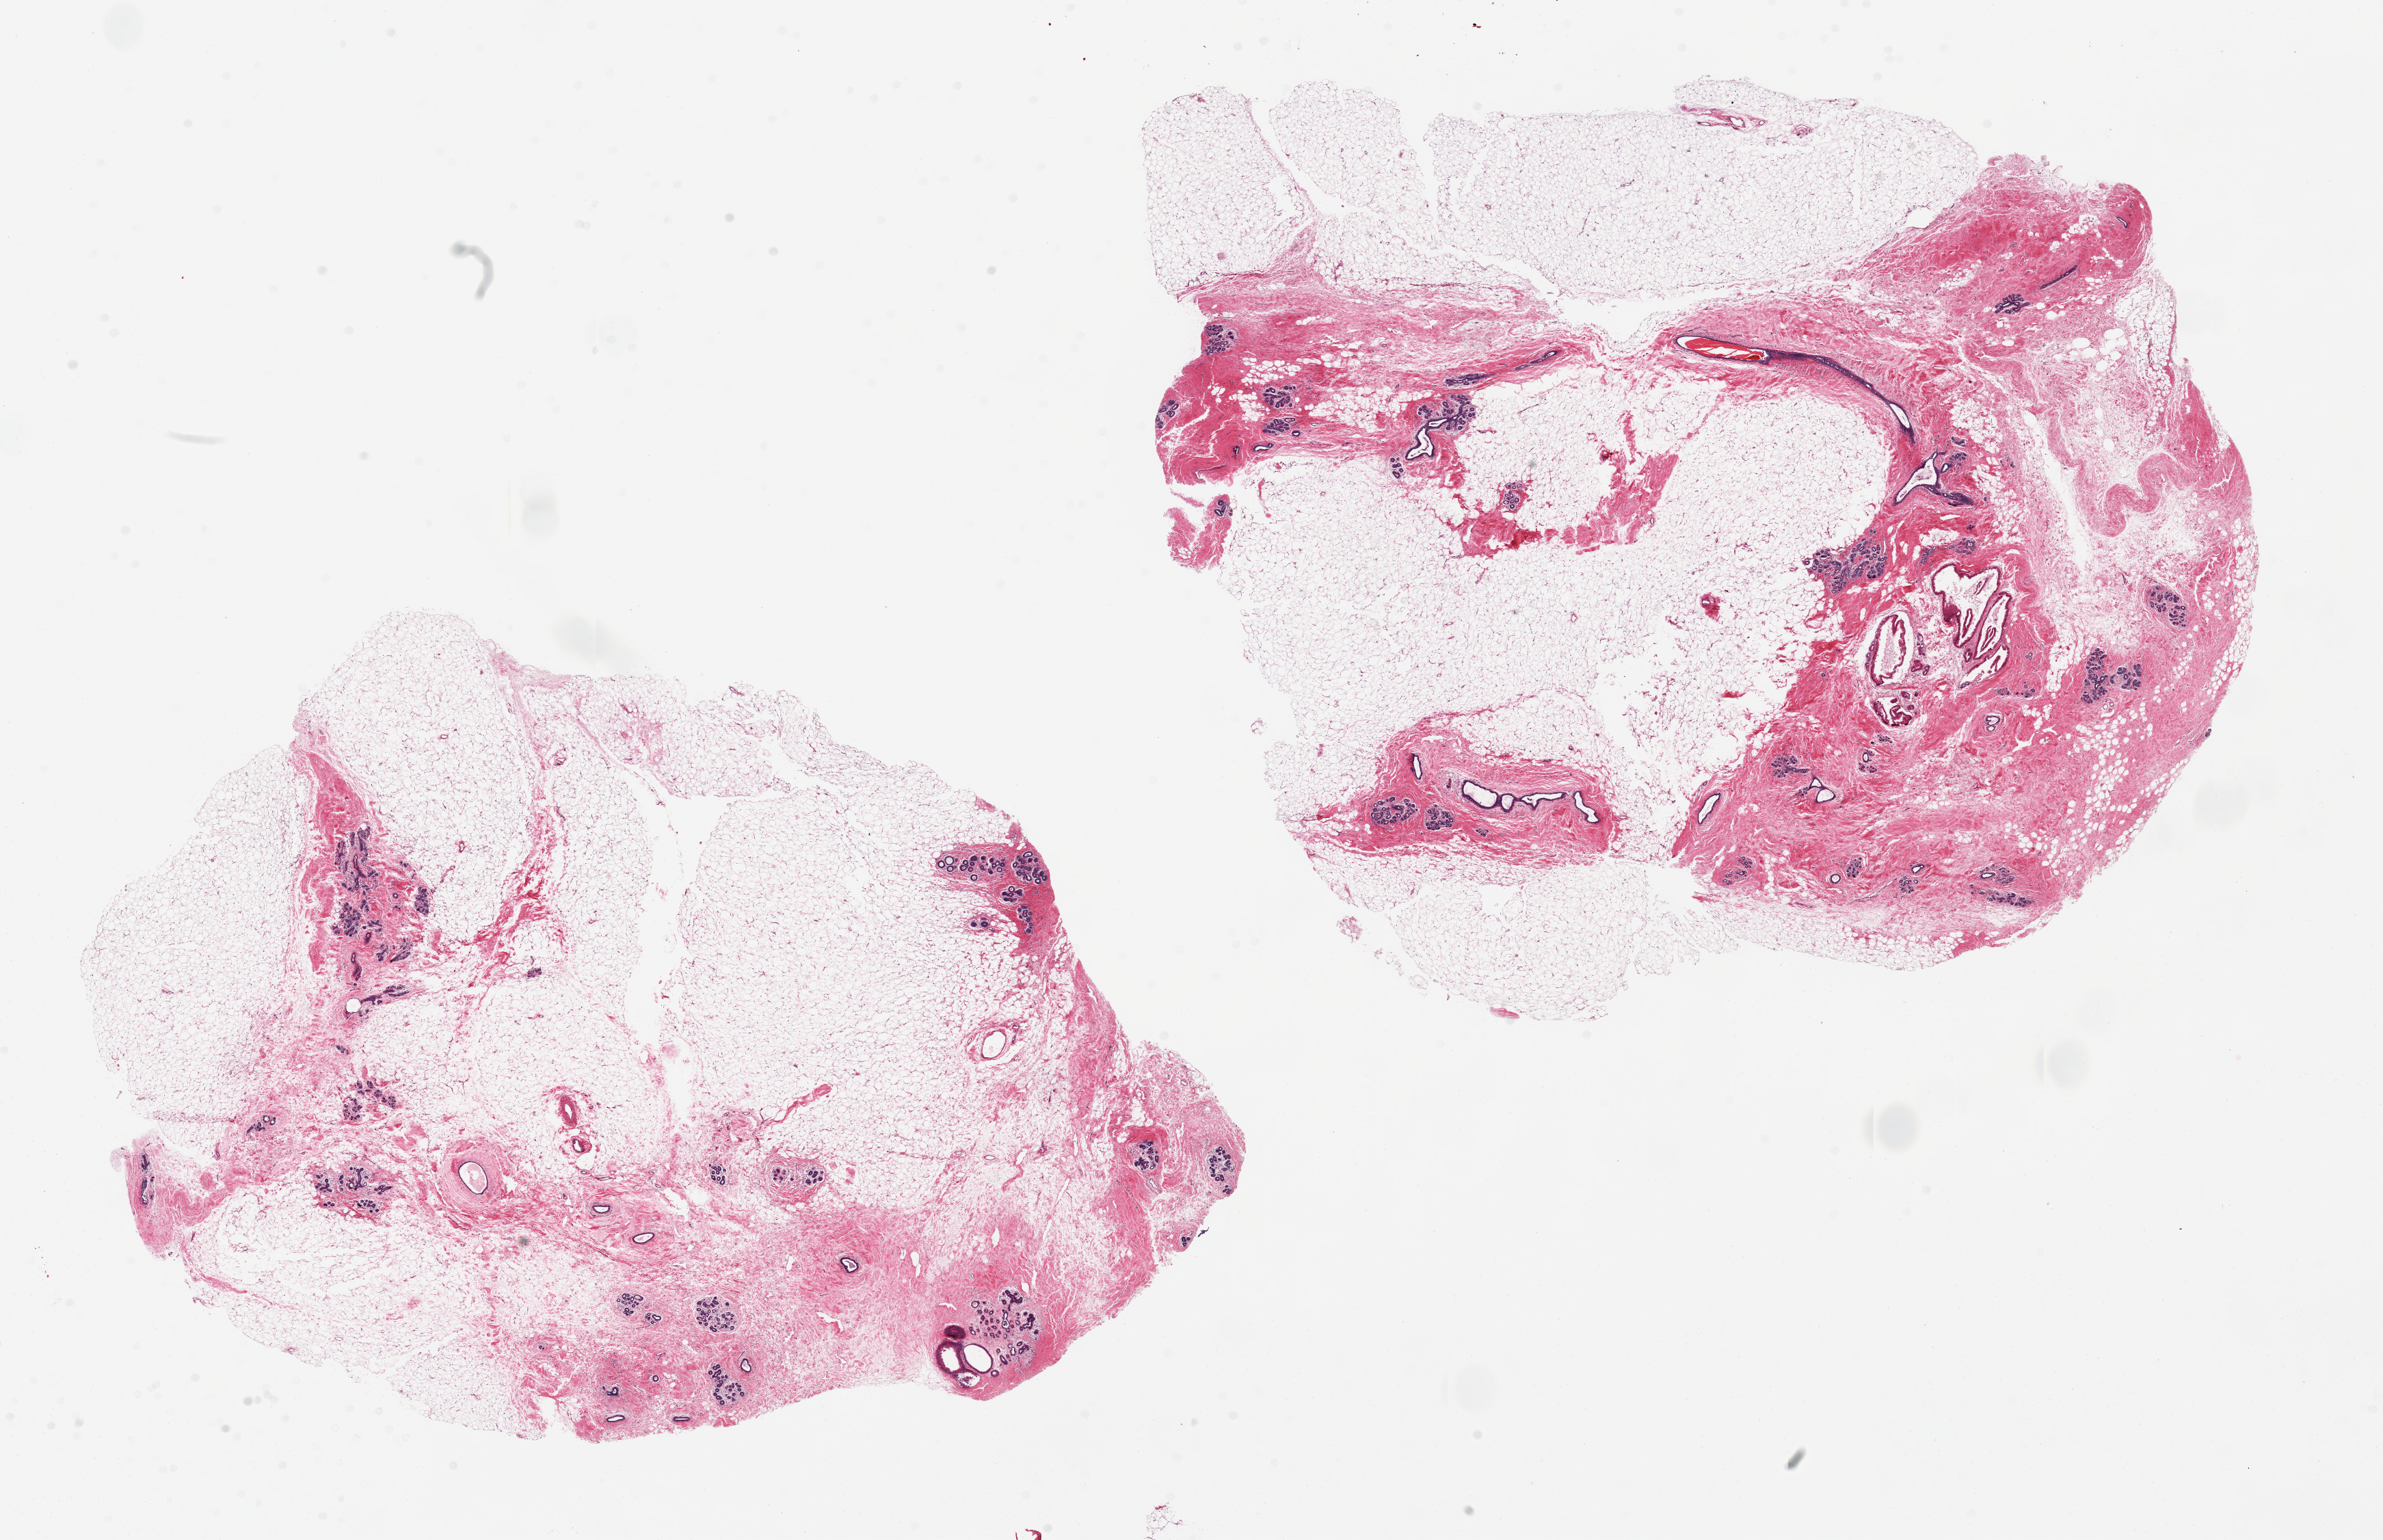
Whole-slide image, hematoxylin and eosin (H&E) stain — a low-resolution overview of the entire scanned area, about 27.6 x 17.8 mm (from a 20x scan), PAXgene-fixed paraffin-embedded (PFPE) section, sampled site (target tissue): breast, donor tissue sample. Donor: female.
• review note (as recorded): 2 pieces. 14x10 & 13x11mm; Ducts and lobules present. Adipose is 50-60%